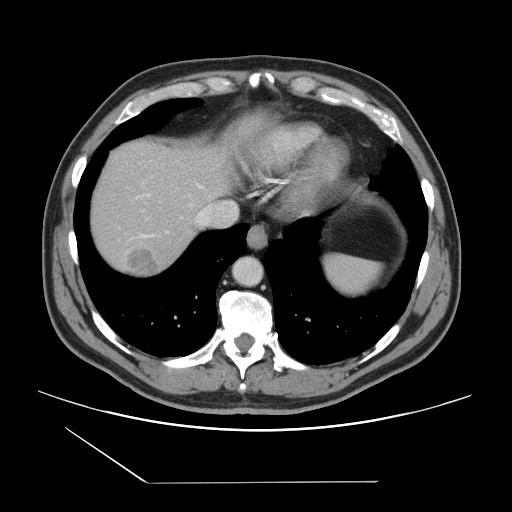
Contrast-enhanced abdominal CT, one axial slice; position 129 of 157 along the scan axis; 120 kVp; intravenous contrast given; soft-tissue window (W 400 / L 40 HU); 512 × 512 image matrix, field of view 407 × 407 mm. Male patient, age 61 years. Case-level facts recorded for this patient, not image findings: diagnosis: colorectal cancer liver metastases, imaged before liver resection; multiple liver metastases: yes; largest metastasis: 5.5 cm; disease in both lobes: yes.
Outlined on this slice (manually delineated by an expert):
- hepatic veins: bounding box (x1, y1, x2, y2) in pixels: (139, 201, 239, 238)
- liver: (89, 139, 232, 279)
- planned liver remnant (the part of the liver to remain after resection): (89, 139, 226, 232)
- liver metastasis: (127, 245, 161, 276)